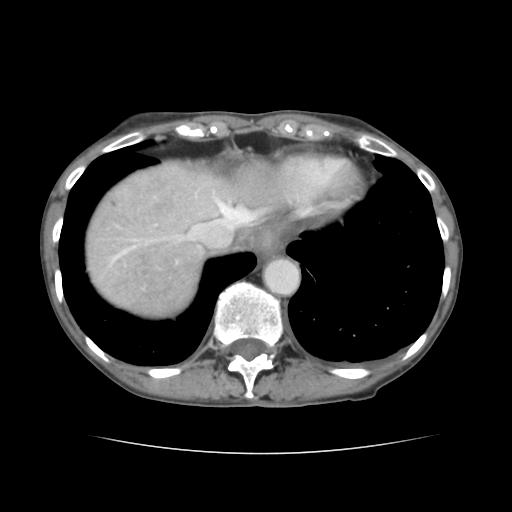
Contrast-enhanced abdominal CT, one axial slice; position 124 of 136 along the scan axis; 120 kVp; intravenous contrast given; soft-tissue window (W 400 / L 40 HU); 512 × 512 image matrix, field of view 319 × 319 mm. Female patient, age 77 years. Case-level facts recorded for this patient, not image findings: diagnosis: colorectal cancer liver metastases, imaged before liver resection; multiple liver metastases: yes; largest metastasis: 3 cm; disease in both lobes: no.
Structures marked on this image (manually delineated by an expert):
- hepatic veins: bounding box [x1, y1, x2, y2] px = [110, 191, 261, 263]
- liver: [85, 161, 285, 316]
- planned liver remnant (the part of the liver to remain after resection): [187, 161, 284, 228]